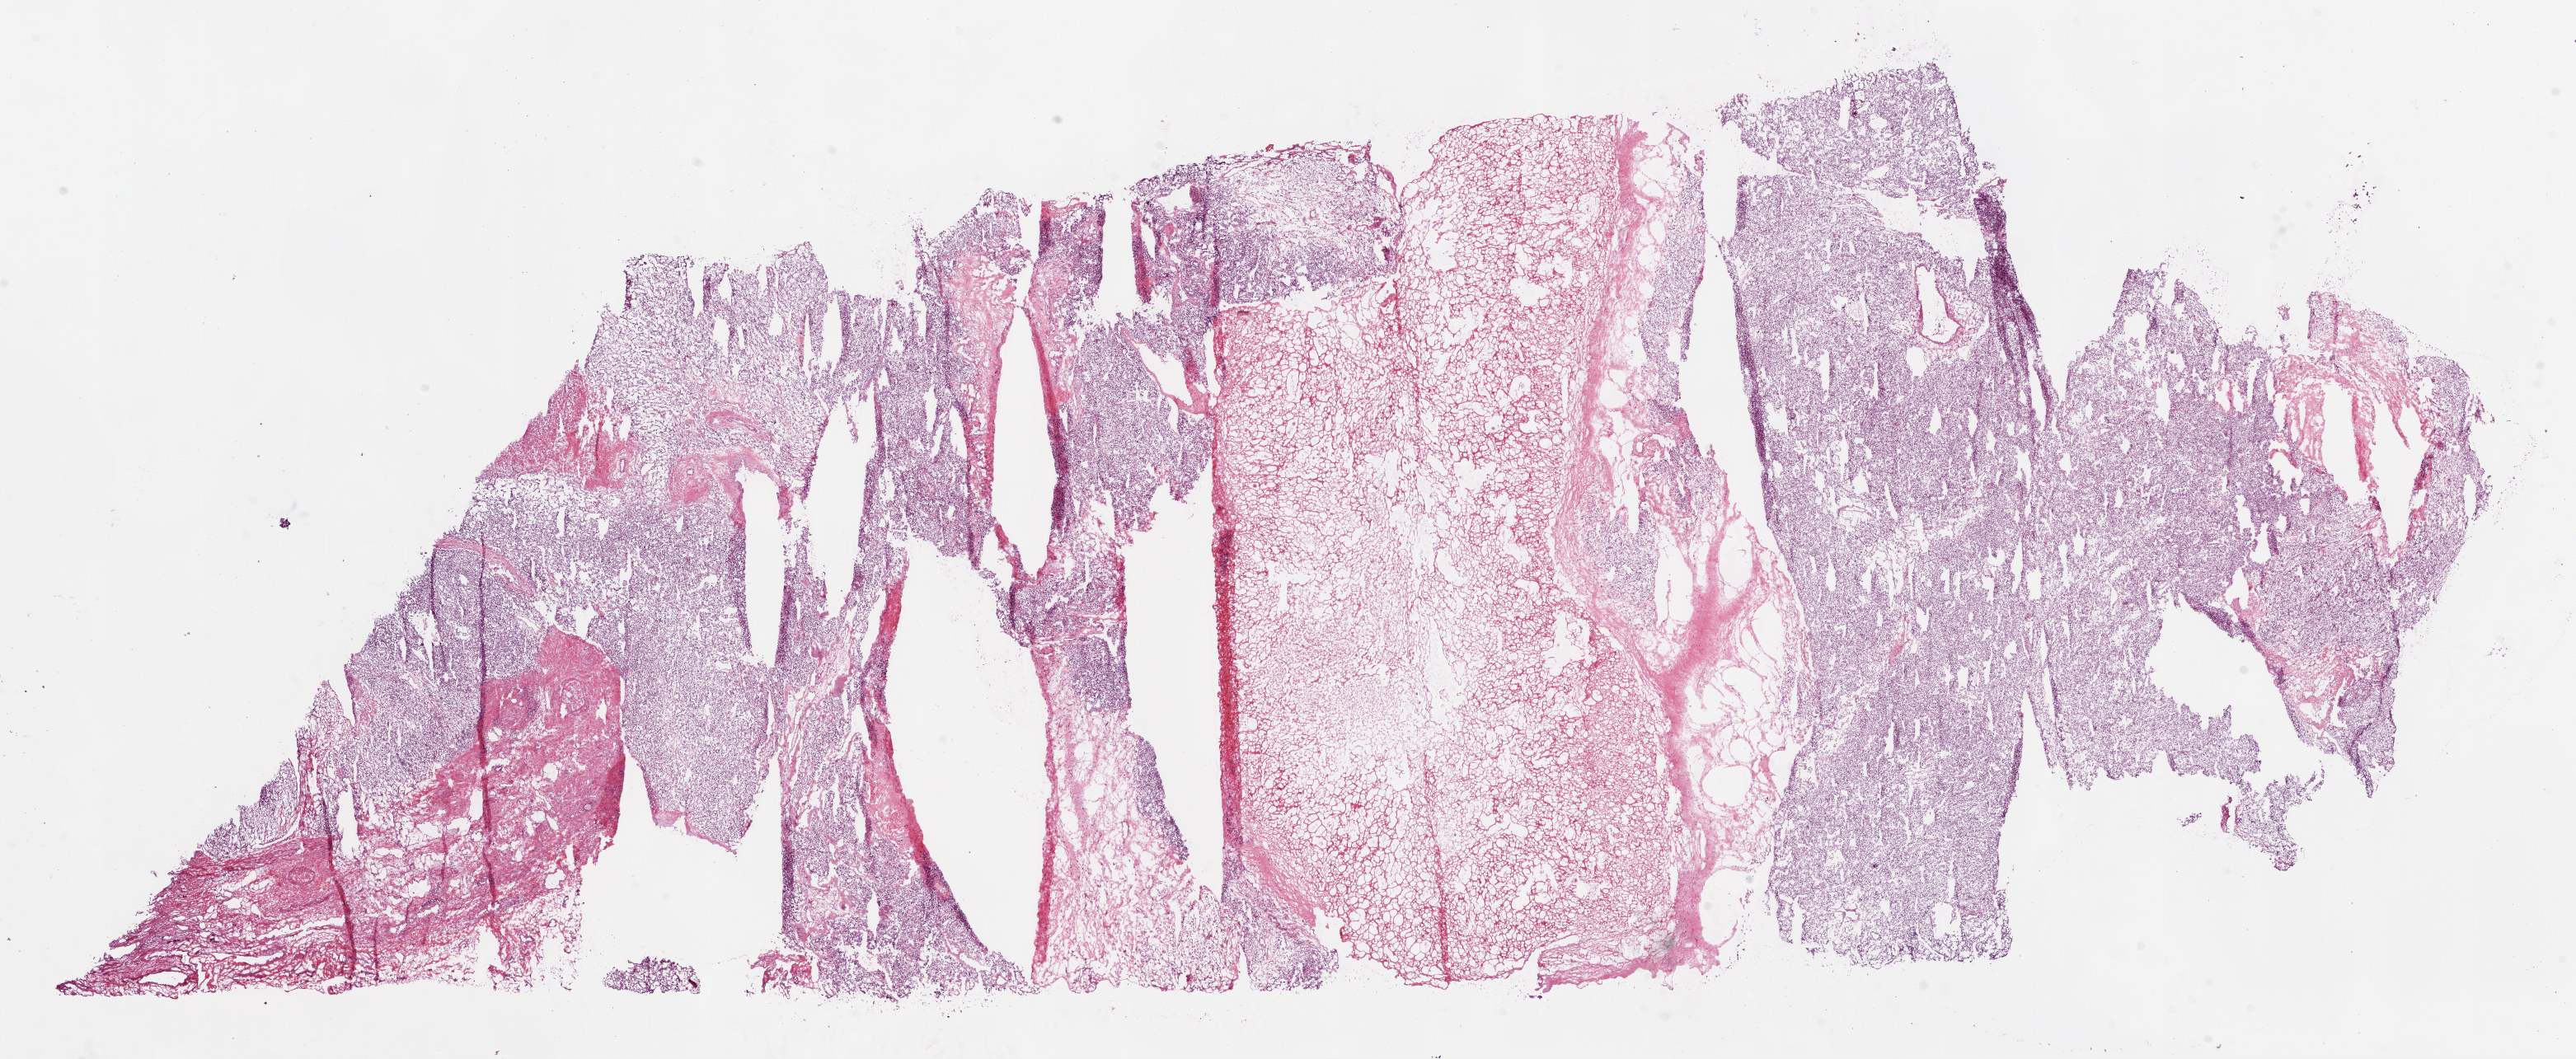
H&E whole-slide image — shown as a low-resolution overview of the whole scanned area (about 25.1 x 10.3 mm, slide scanned at 20x), frozen section, kidney, primary tumour sample. Female patient; age at initial diagnosis 79 years. Pathologist review of this section (percent, as recorded): tumour cells 60%, tumour nuclei 80%.
Pathologic diagnosis: Clear cell adenocarcinoma, NOS.